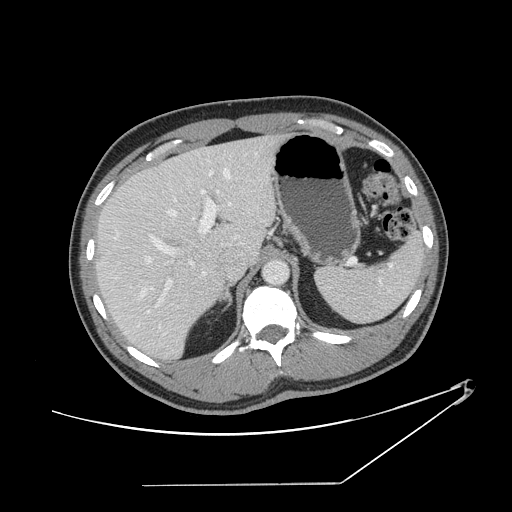
Contrast-enhanced abdominal CT, one axial slice. Position 98 of 152 along the scan axis. Reconstruction kernel STANDARD. 120 kVp. Intravenous contrast given. Soft-tissue window (W 400 / L 40 HU). 512 × 512 image matrix, field of view 432 × 432 mm. Male patient, age 45 years. Case-level facts recorded for this patient, not image findings: diagnosis: colorectal cancer liver metastases, imaged before liver resection; multiple liver metastases: no; largest metastasis: 1 cm; disease in both lobes: no.
Annotated regions visible in this slice (outlined manually by an expert reader):
- hepatic veins: bounding box (x1, y1, x2, y2) in pixels: (111, 160, 232, 297)
- liver: (98, 137, 279, 358)
- planned liver remnant (the part of the liver to remain after resection): (98, 154, 230, 358)
- portal vein (with intrahepatic branches): (136, 171, 216, 329)